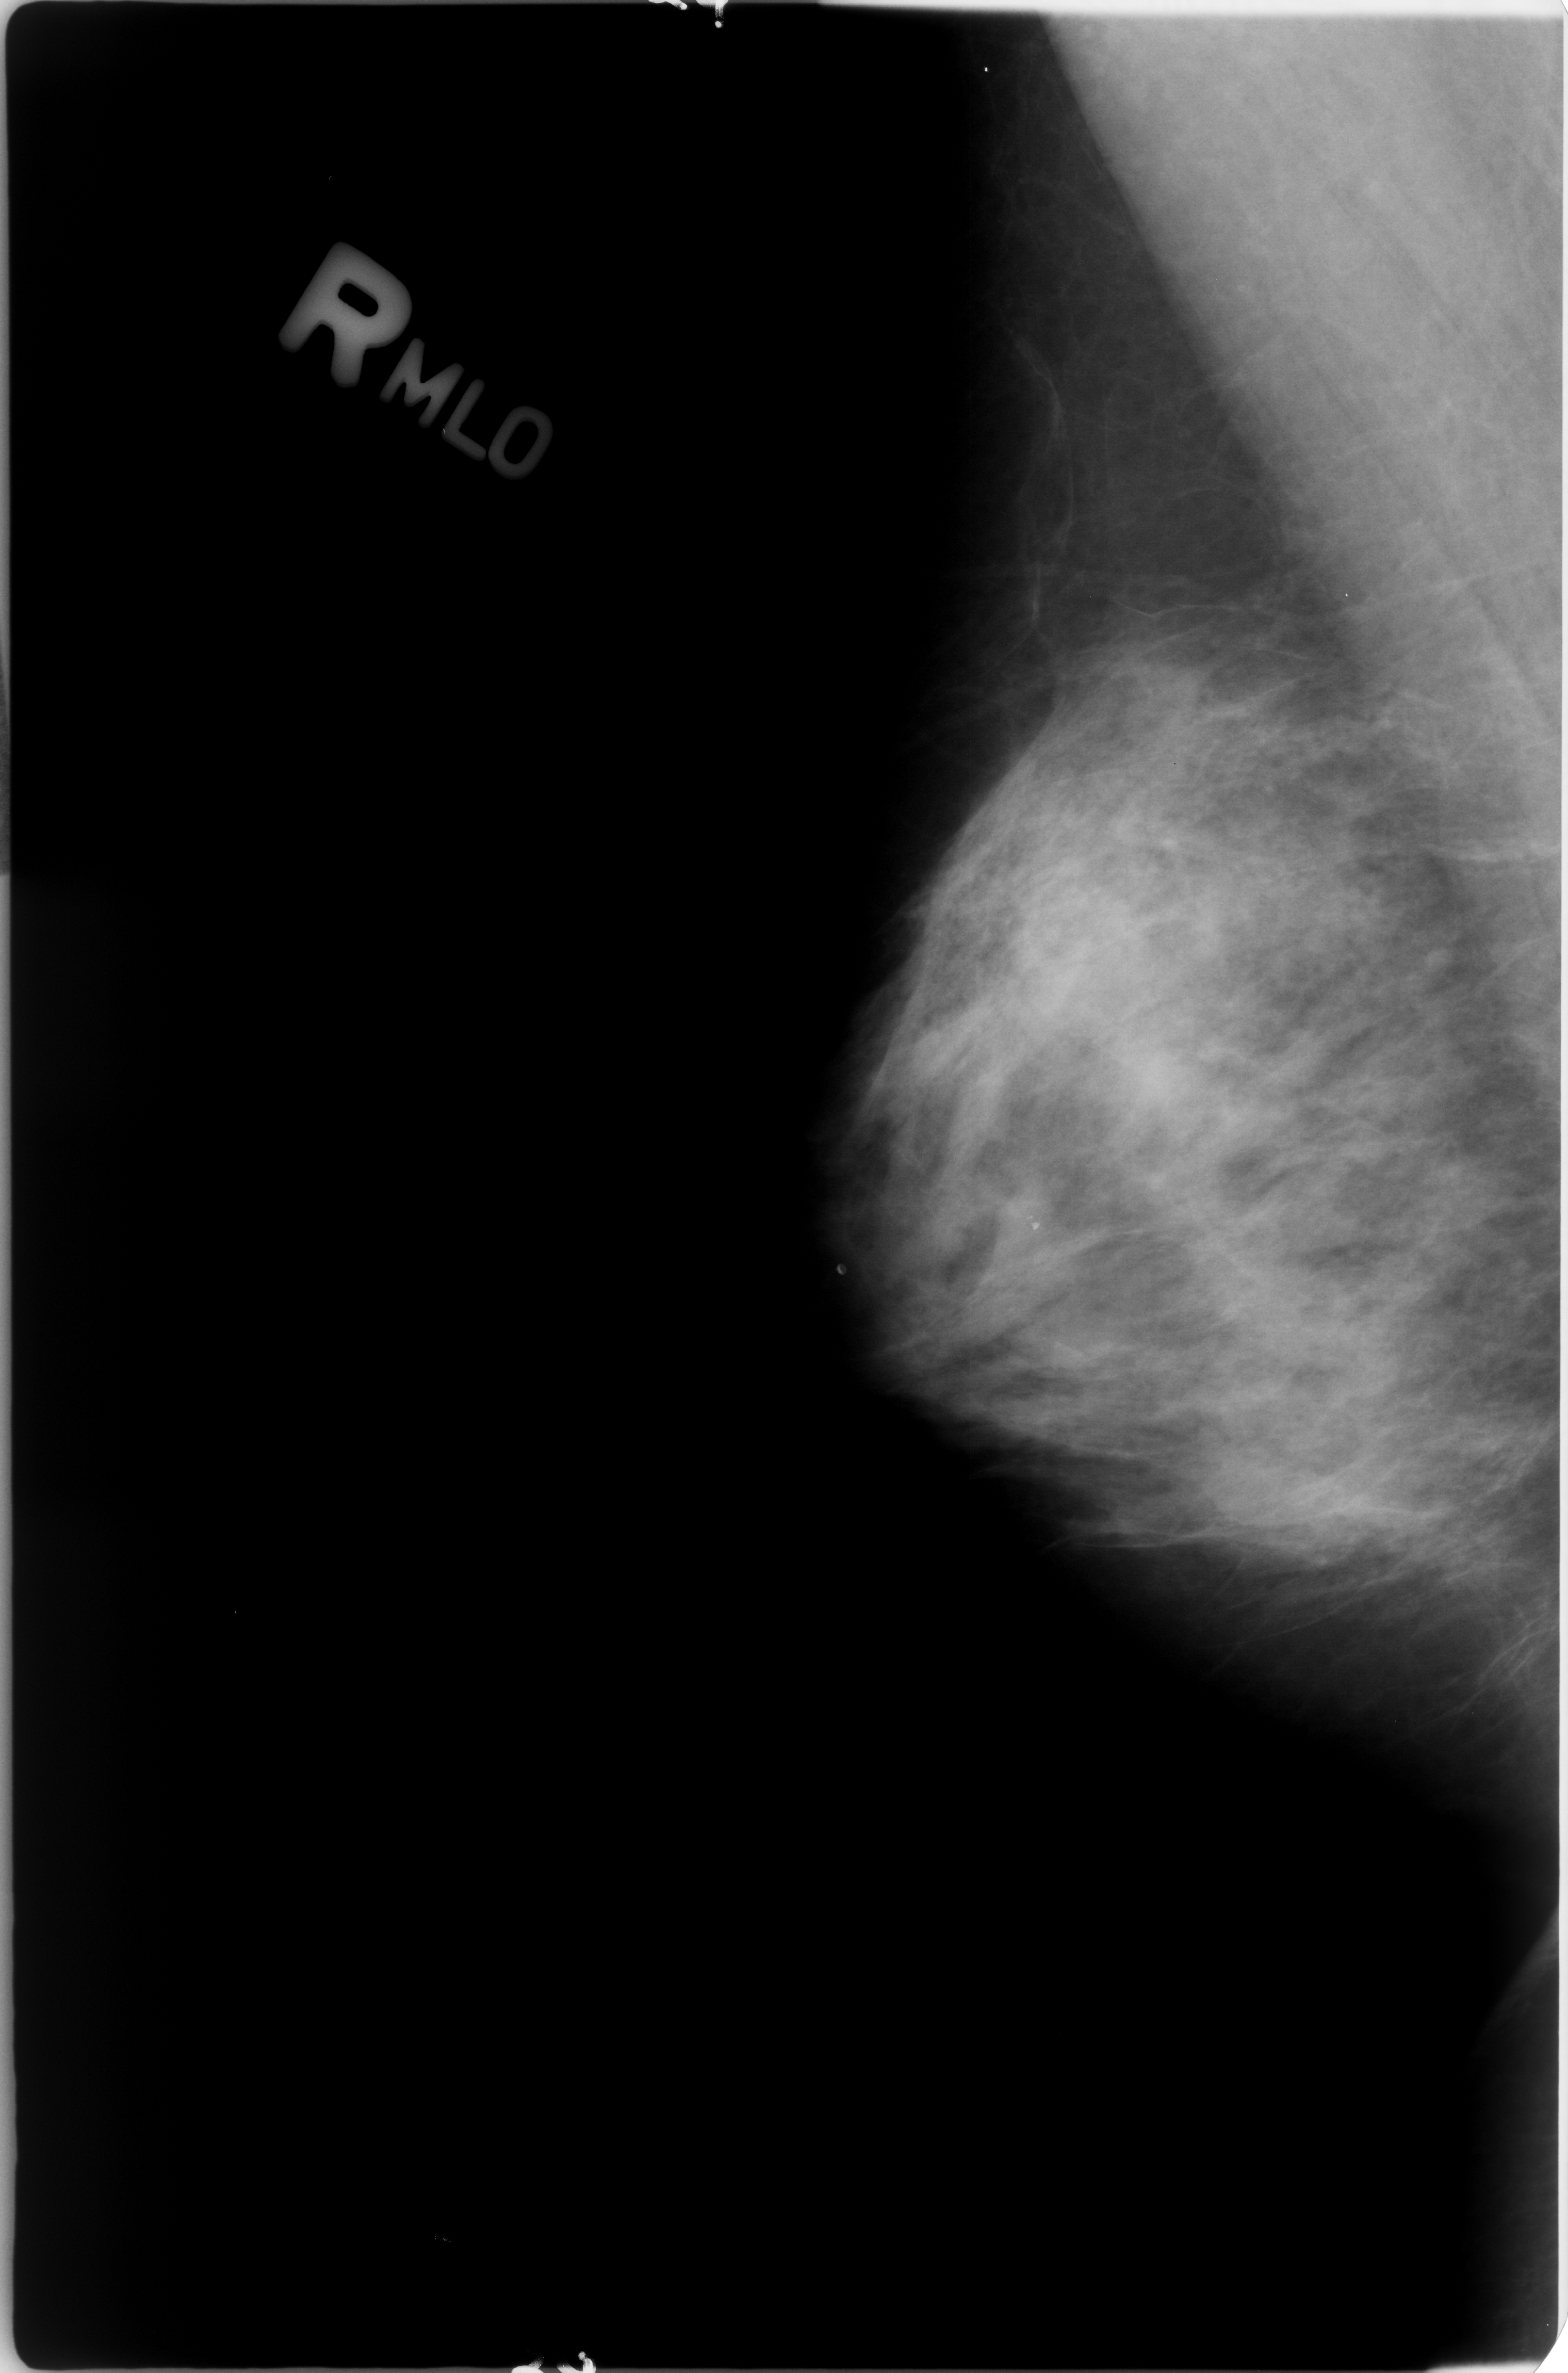
Digitized screen-film mammogram. Right breast. MLO view. BI-RADS breast density category 3 (scale 1–4). 1568 × 2373 image matrix.
Marked abnormalities (boxes around the expert regions of interest):
- Finding 1 of 2: calcifications, morphology lucent center; BI-RADS assessment category 2; subtlety rating 3 on a 1 (subtle) to 5 (obvious) scale; benign; no additional work-up was recommended (outcome (as recorded, no biopsy): benign without callback): bounding box (x1, y1, x2, y2) in pixels: (833, 1217, 892, 1284)
- Finding 2 of 2: calcifications, morphology coarse; BI-RADS assessment category 2; benign; no additional work-up was recommended (outcome (as recorded, no biopsy): benign without callback): (1019, 1209, 1049, 1243)